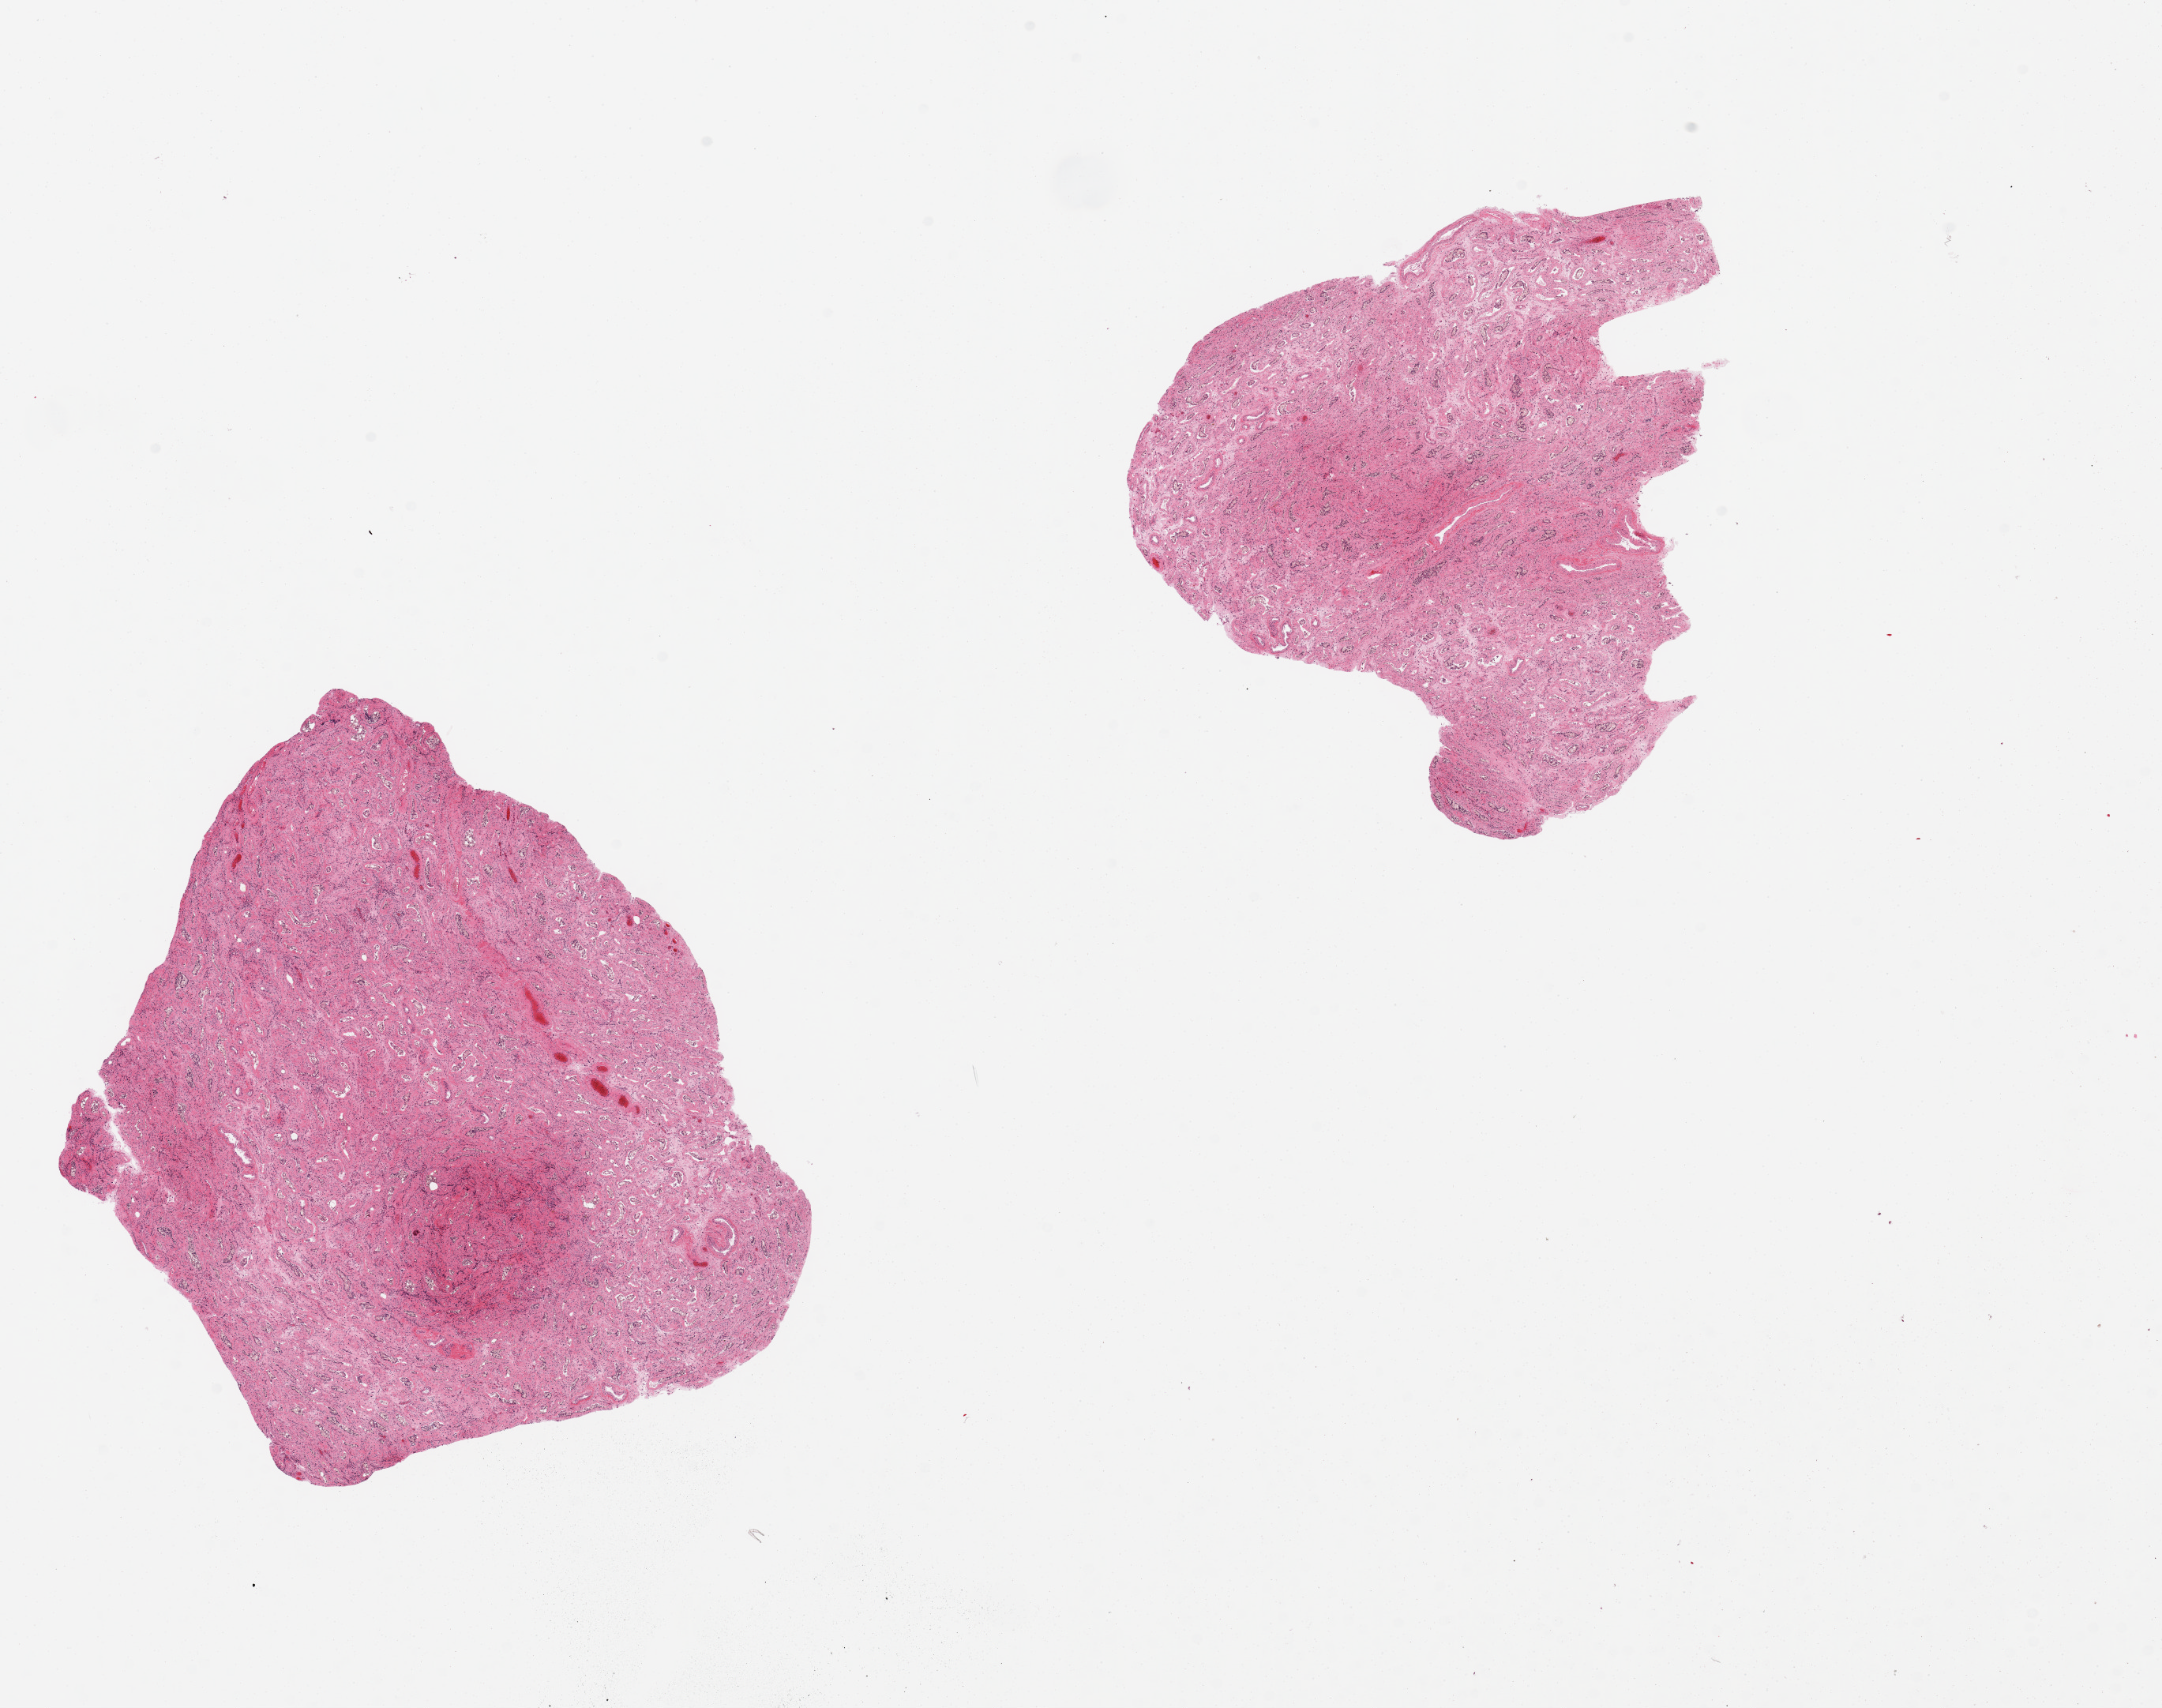
Digitized hematoxylin and eosin (H&E)-stained section — a low-resolution overview of the entire scanned area, about 21.7 x 17.1 mm (from a 20x scan), PAXgene-fixed paraffin-embedded (PFPE) section, target tissue: testis, tissue donor sample. Male donor.
- review note (as recorded): 2 pieces, markedly hyalinized, no evidence of spermatogensis. Marked autolysis